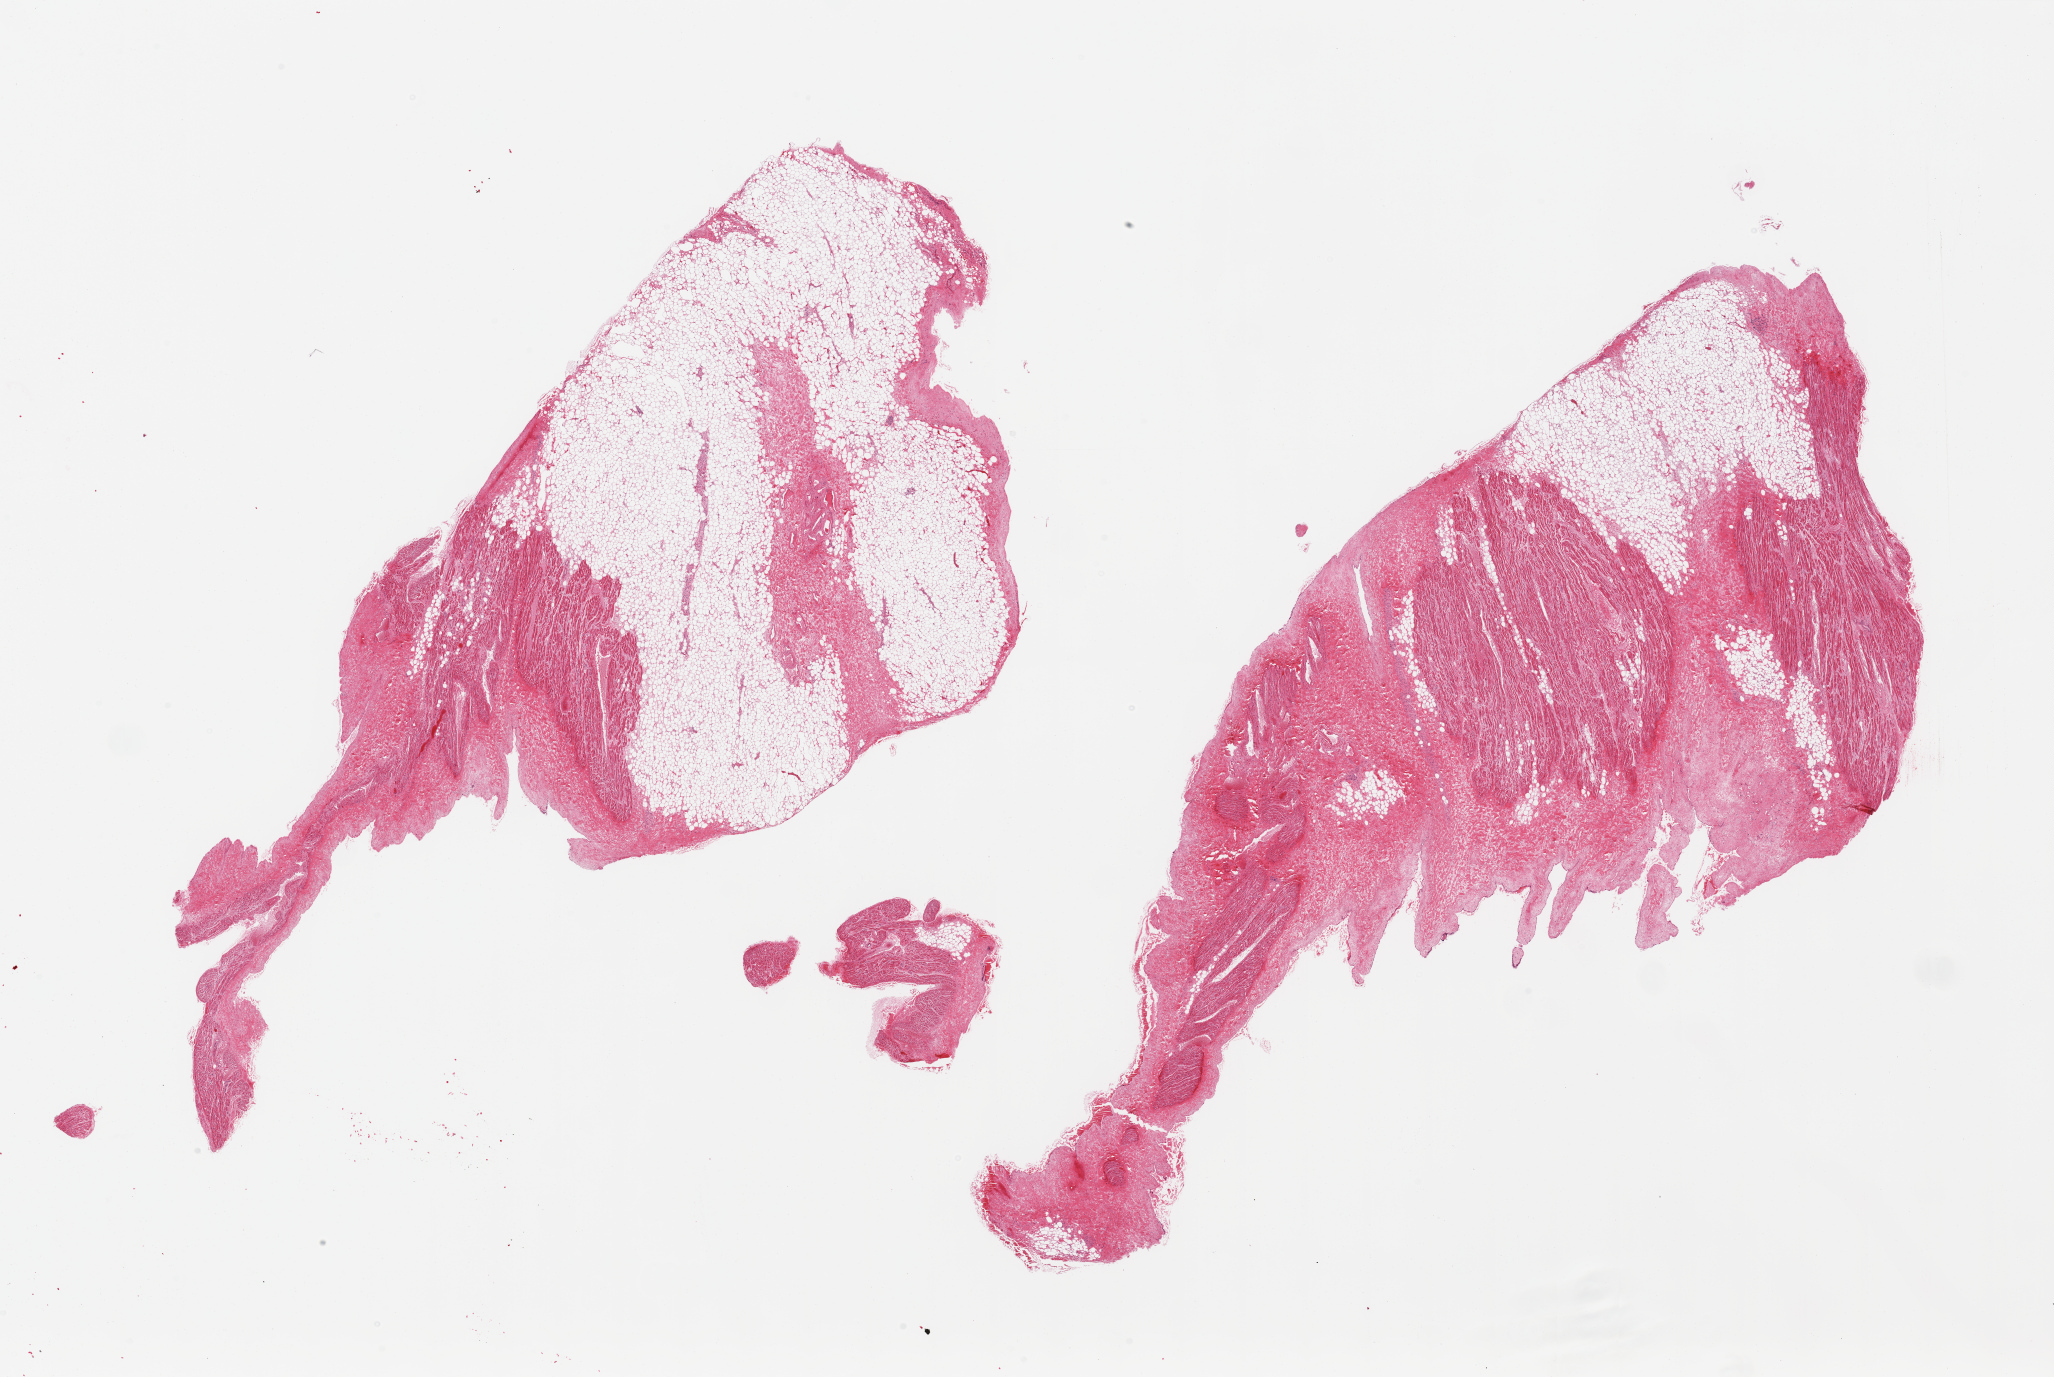
Whole-slide image, haematoxylin and eosin stain — low-resolution overview of the scanned area, about 32.5 x 21.8 mm (from a 20x scan). PAXgene-fixed, paraffin-embedded tissue. Target tissue: auricular appendage. Tissue donor sample. Donor sex: male.
Reviewer comment on this tissue sample: 2 pieces, no abnormalities; ~30-40% interstitial fat.